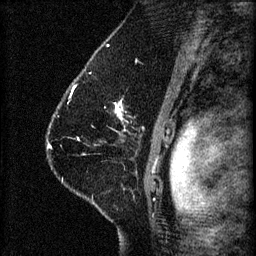
Breast MRI (dynamic contrast-enhanced), one sagittal slice. Slice 45 of 60 in the series (ordered by position). 3 images stored at this slice position (order not interpretable as contrast timing). 1.5 T. TE 4.2 ms, TR 8.2 ms. 2 mm slice thickness. 256 × 256 image matrix, field of view 180 × 180 mm. Female patient, age 41 years.
Outlined on this slice (semi-automatic segmentation, software-assisted and operator-edited):
- analysis volume of interest (the breast-tissue region the enhancement analysis was run in; not a lesion): bounding box (x1, y1, x2, y2) in pixels: (70, 94, 165, 173)
- tumour enhancement mask (voxels above the 70 % enhancement threshold inside the analysis volume of interest): (114, 100, 123, 121)